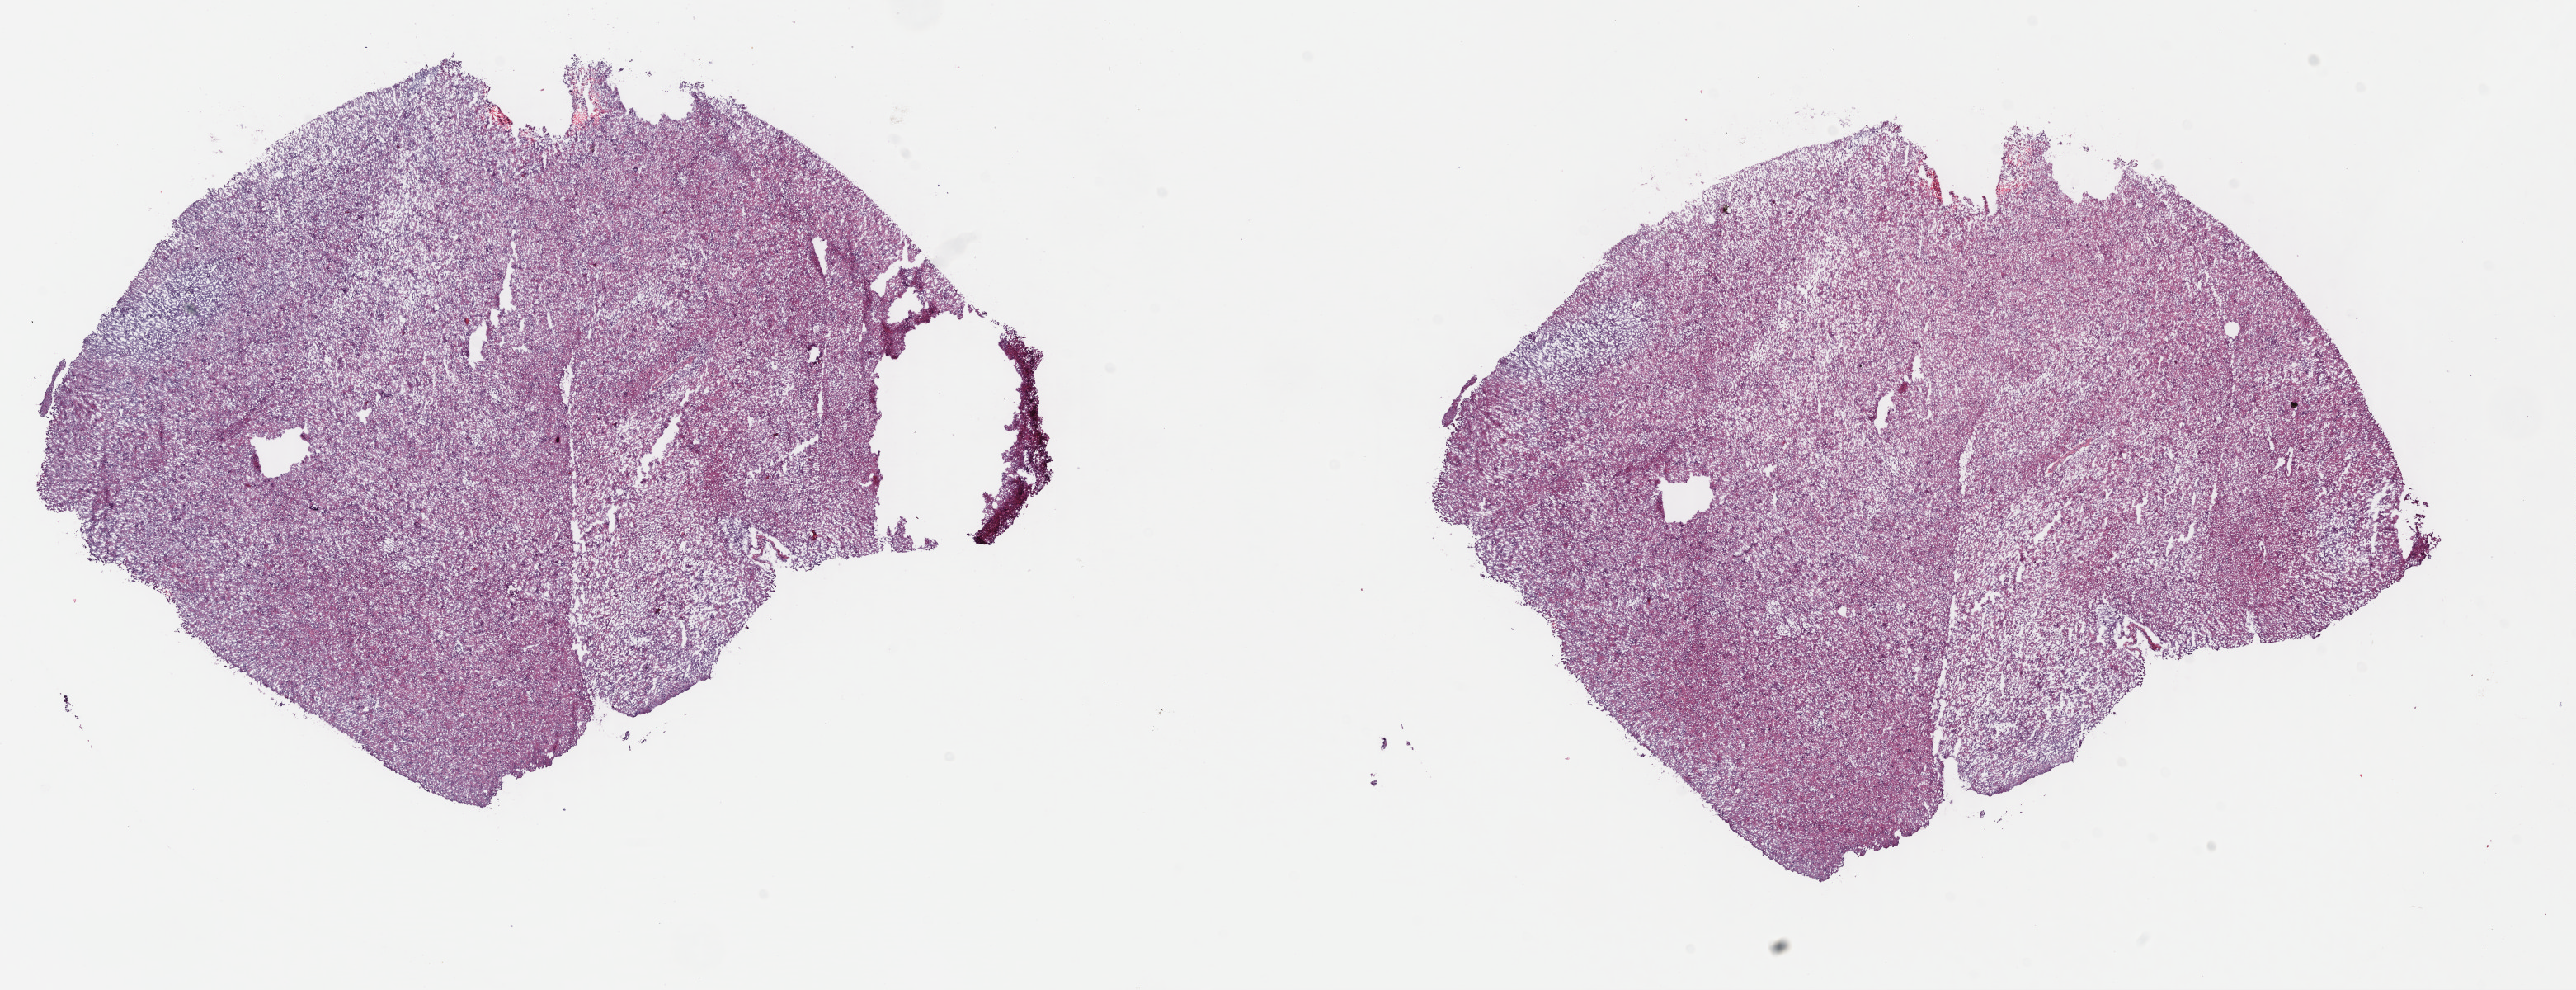
Whole-slide histology image, H&E-stained, whole scanned area (about 24.6 x 9.4 mm, from a 40x scan) shown as a low-resolution overview. Frozen section. Sample: primary tumour, brain. Male, age 41 years at initial diagnosis. Pathologist review of this section (percent, as recorded): tumour cells 35%, tumour nuclei 80%.
Histologic diagnosis: Astrocytoma, anaplastic (cerebrum).